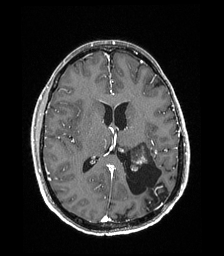
Brain MRI from a brain-tumour surgery series, one axial slice. Position 88 of 192 along the scan axis. T1-weighted post-contrast. 224 × 256 image matrix. From the clinical record (not read from this slice): histopathology: Low grade glioma; IDH mutation: no; tumour location: Left Parieto-Occipital Intraventricular.
Annotated regions visible in this slice (expert manual segmentation):
- previous resection cavity: box from (x=126, y=152) to (x=165, y=204) px
- tumour: (x=130, y=143)–(x=151, y=171)